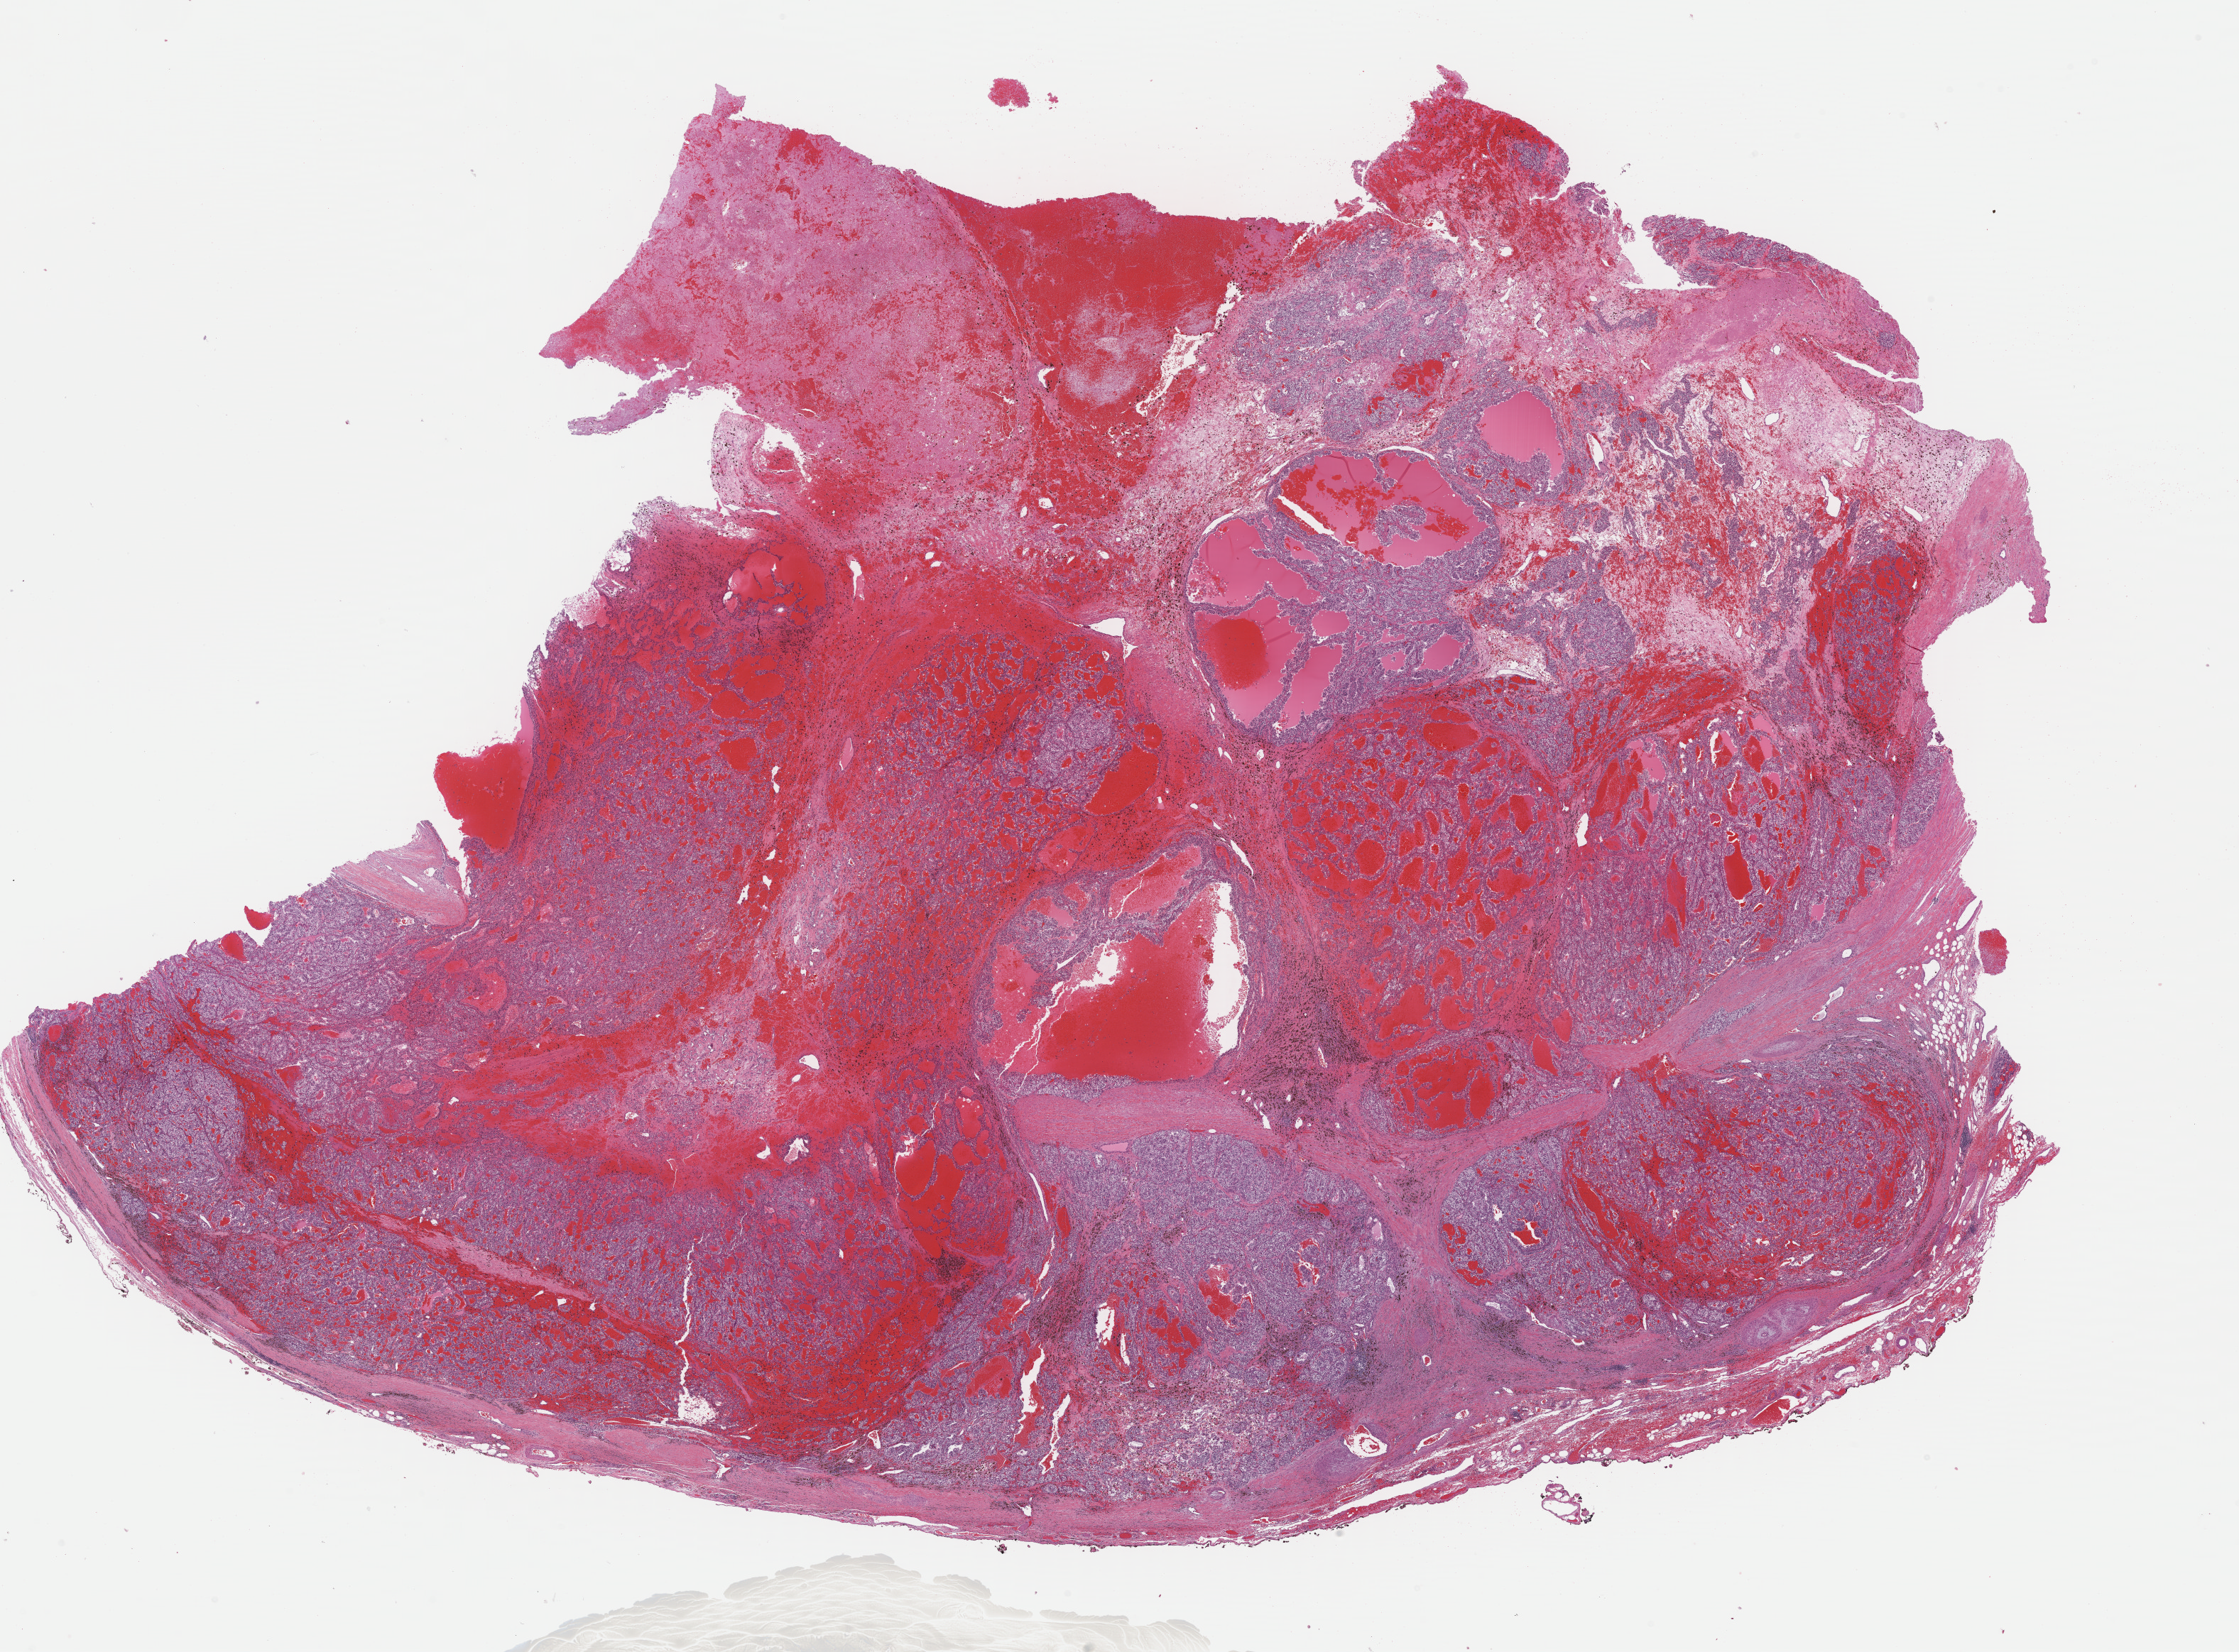
Whole-slide histology image, H&E — a low-resolution overview of the entire scanned area, about 24.9 x 18.4 mm (slide scanned at 40x). FFPE section. Kidney, primary tumour sample. Male patient; age at initial diagnosis 55 years. Histologic grade: G3 (poorly differentiated).
* histologic diagnosis: Clear cell adenocarcinoma, NOS
* AJCC pathologic stage: I (6th edition)
* TNM: T1b NX MX